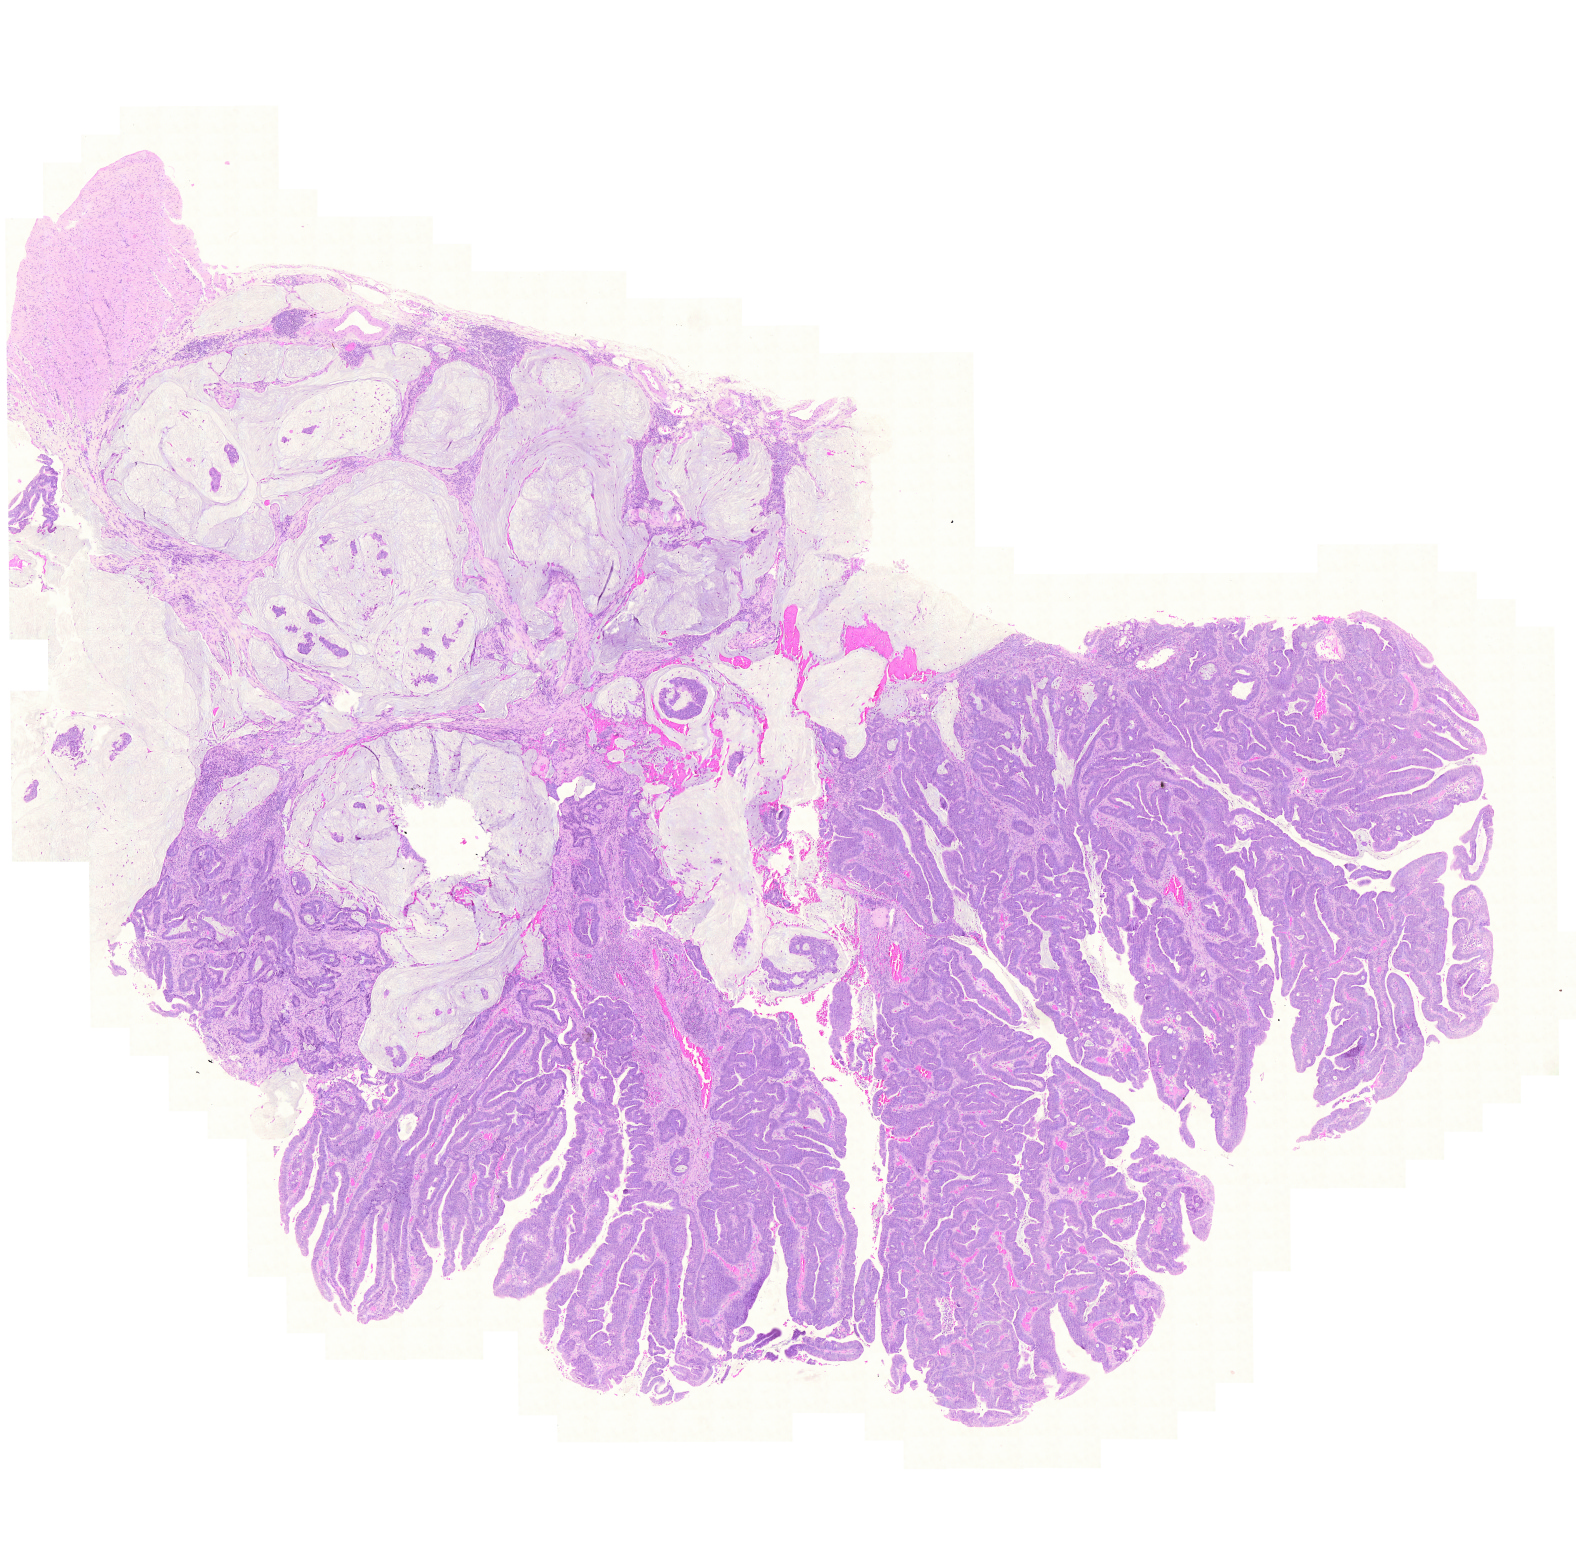
Whole-slide histology image, Hematoxylin and eosin (H&E) stained, shown as a low-resolution overview of the whole scanned area (about 11.7 x 11.5 mm, slide scanned at 20x). Formalin-fixed paraffin-embedded (FFPE) diagnostic section. Rectum, primary tumour sample. Patient: male, age at initial diagnosis 67 years.
• AJCC pathologic stage: II (5th edition)
• diagnosis: Adenocarcinoma, NOS